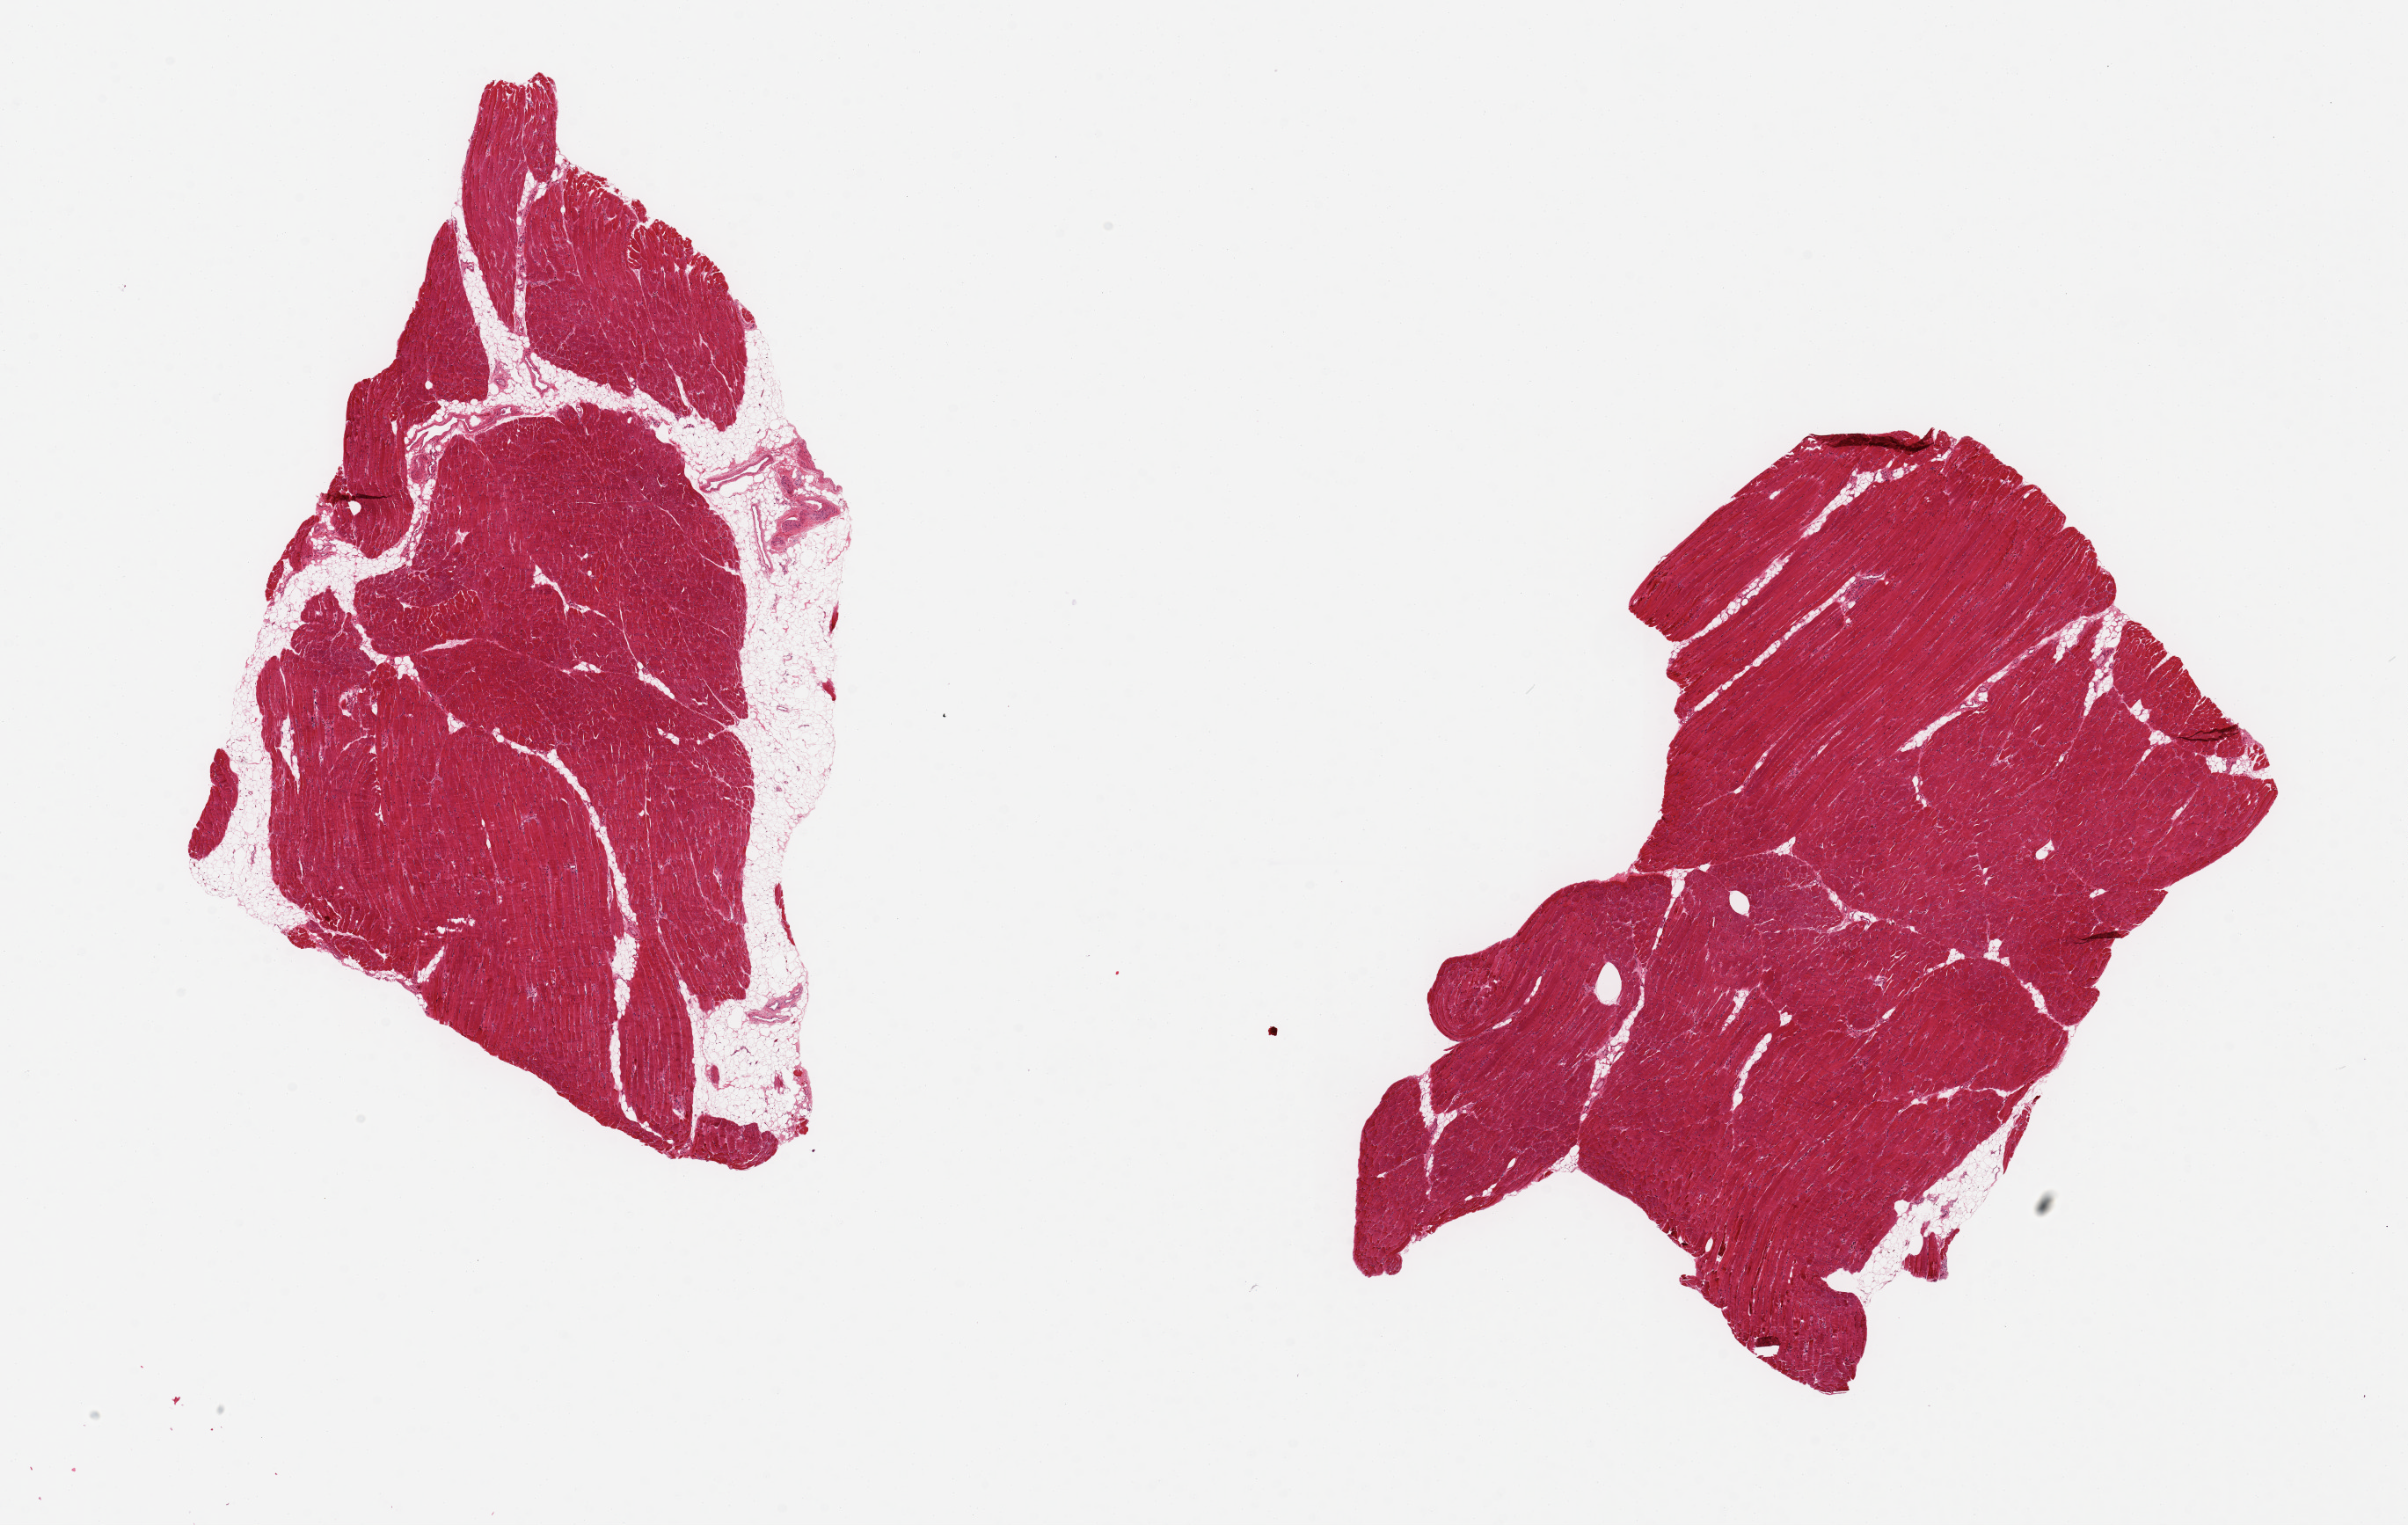
Digitized H&E-stained section — low-resolution overview of the scanned area, about 21.7 x 13.7 mm (acquisition: 20x scan); PAXgene-fixed, paraffin-embedded tissue; section of skeletal muscle (target tissue); donor tissue sample.
- reviewer comment on this tissue sample: 2 pieces ~8x5mm, minimal interstitial fat; one with ~10% adherent fat